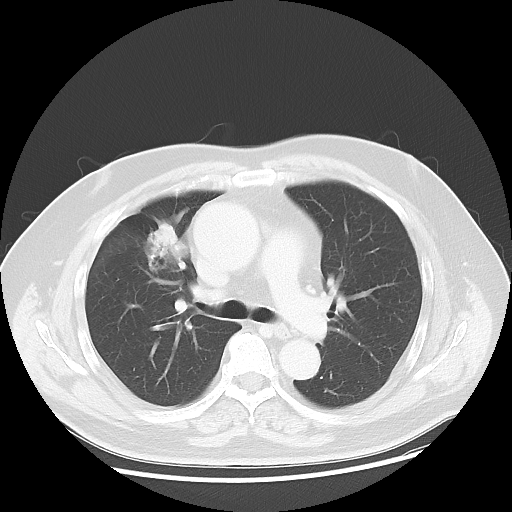
Chest CT, one axial slice; slice 28 of 48 in the series (ordered by position); reconstruction kernel LUNG; 120 kVp; lung window (W 1500 / L -600 HU); 512 × 512 image matrix, field of view 392 × 392 mm. Male patient, age 60 years. From the clinical record (not read from this slice): clinical TNM (as recorded): T2 N3 M0.
Annotated regions visible in this slice (bounding box drawn by a radiologist):
- lung tumour (recorded histology: adenocarcinoma): bounding box <139,213,189,288> (left, top, right, bottom; pixels)